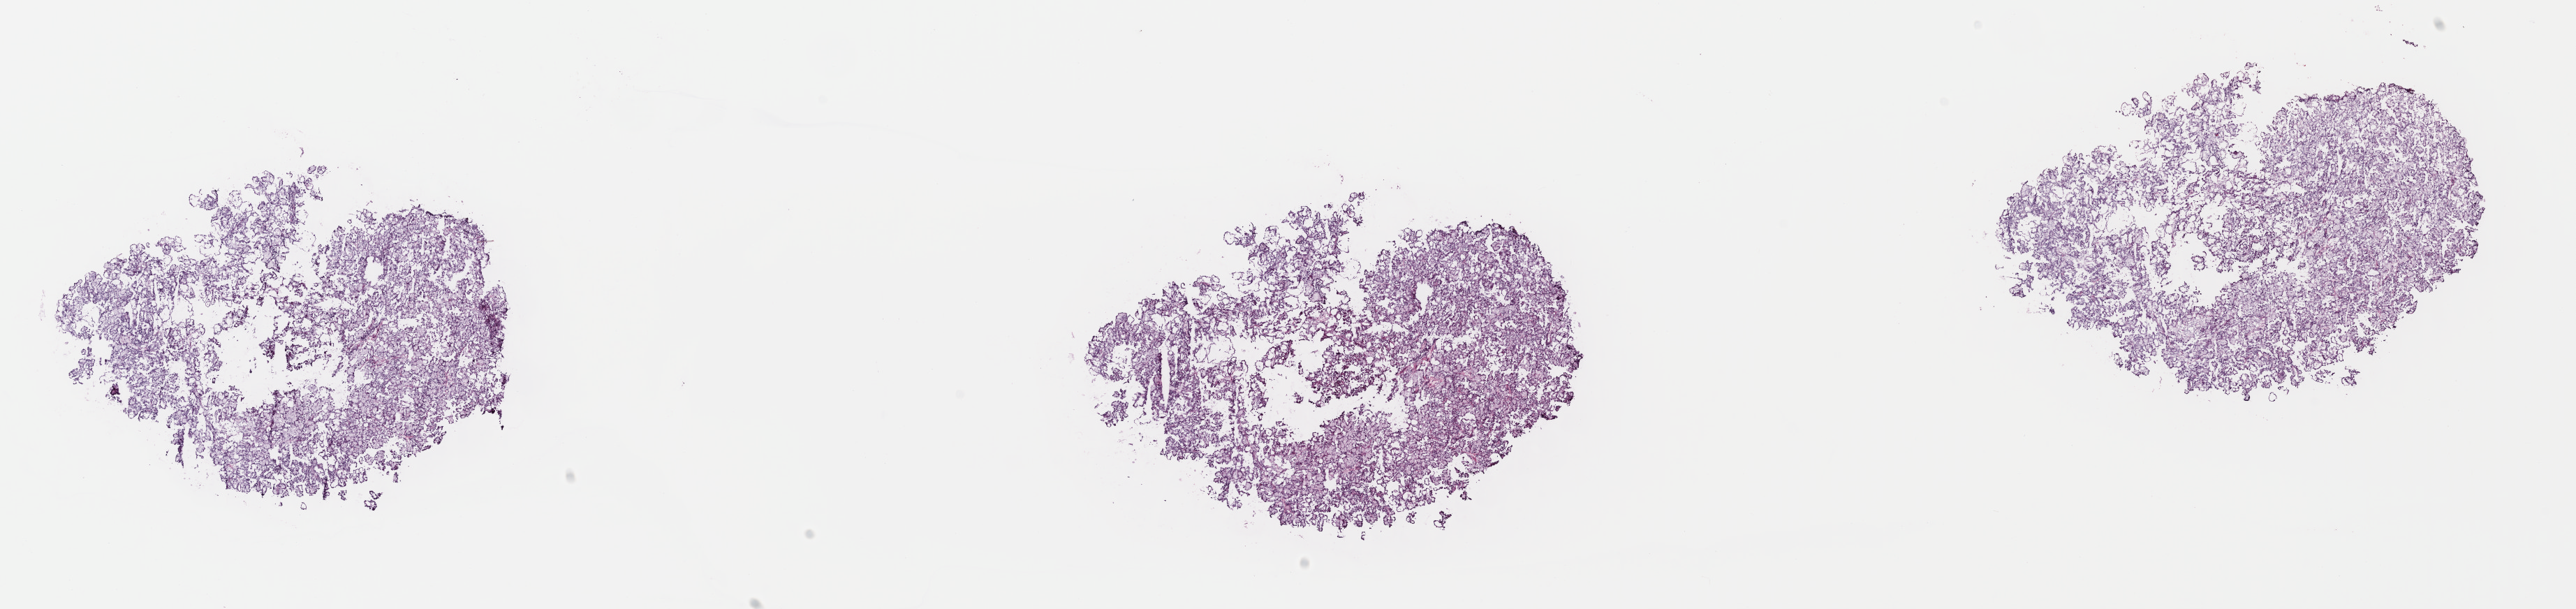
H&E-stained whole-slide image, low-resolution overview of the scanned area, about 29.0 x 6.9 mm (from a 40x scan); frozen section; sample: primary tumour, kidney. Patient: male, age at initial diagnosis 80 years. Slide review estimates, as recorded: tumour cells 75%, tumour nuclei 75%, normal cells 0%, stromal cells 25%, necrosis 0%. Inflammatory infiltration, as recorded: lymphocyte infiltration 0%, monocyte infiltration 10%, neutrophil infiltration 0%.
• histologic diagnosis: Papillary adenocarcinoma, NOS
• AJCC pathologic stage: I (7th edition)